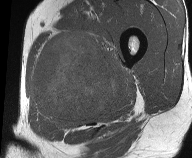
MRI of an extremity soft-tissue mass, one axial slice. Position 26 of 61 along the scan axis. MR volume resampled by the dataset authors to the PET/CT grid (not the native acquisition matrix). 3.27 mm slice thickness. 192 × 158 image matrix, field of view 187 × 154 mm. Male patient. Case-level facts recorded for this patient, not image findings: histological type: pleiomorphic liposarcoma; grade: high; site of the primary tumour: left thigh.
Structures marked on this image (expert contour drawn on MRI and transferred to this co-registered scan by the dataset authors):
- gross tumour volume including surrounding oedema: bounding box [x1, y1, x2, y2] px = [29, 30, 129, 127]
- gross tumour volume (mass): [34, 34, 117, 122]